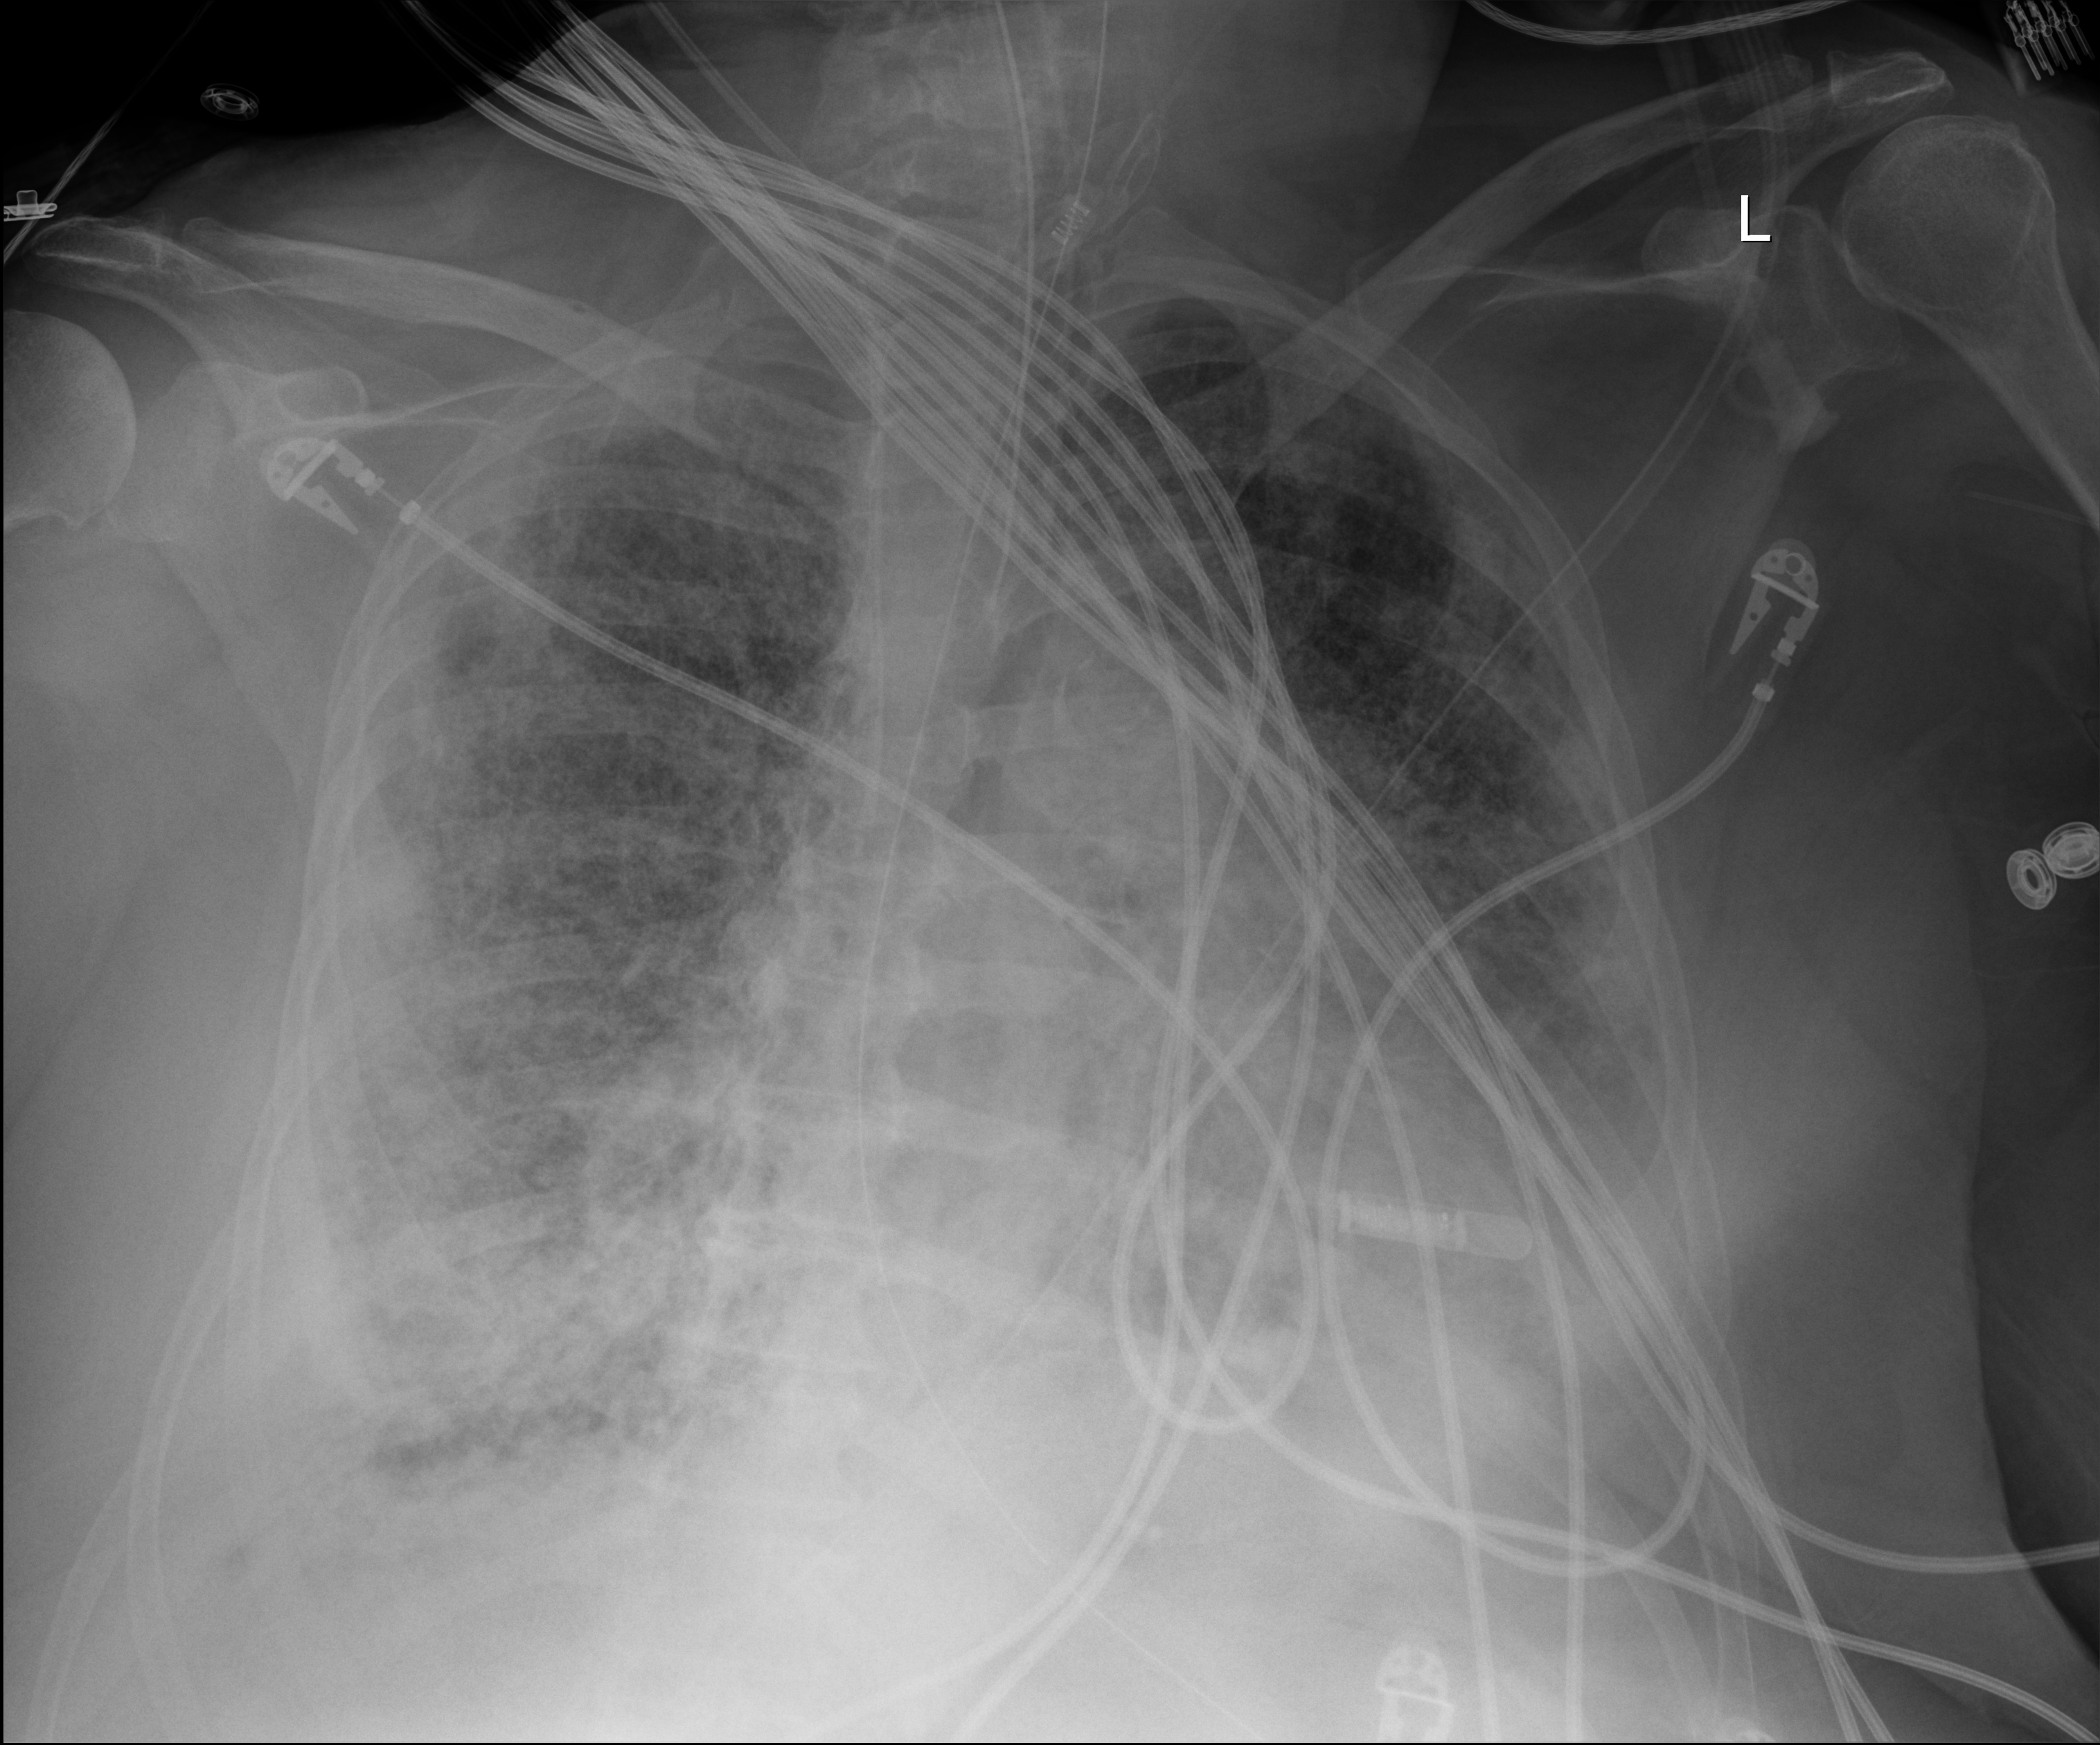
Chest X-ray (portable), anteroposterior (AP) projection. Patient hospitalised with COVID-19; female, aged 60–74 years.
From the hospital-stay record, not from the radiograph (when in the stay this image was taken is not recorded): other chronic lung disease (admission record): yes.